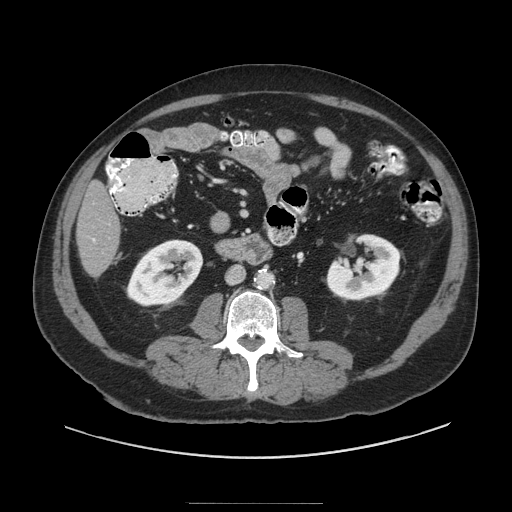
Contrast-enhanced abdominal CT (liver protocol), one axial slice; slice 22 of 91 in the series (ordered by position); soft-tissue window (W 400 / L 40 HU); 512 × 512 image matrix. From the clinical record (not read from this slice): diagnosis: hepatocellular carcinoma (patient treated with transarterial chemoembolisation; whether this scan precedes or follows treatment is not stated here); TNM stage (as recorded): Stage-I; Child-Pugh class: A.
Outlined on this slice (semi-automatically segmented with operator editing):
- liver parenchyma outside the tumour (the mass and vessels are separate outlines, so this box may not span the whole liver): bounding box (x1, y1, x2, y2) in pixels: (76, 180, 120, 276)
- liver vessels: (92, 238, 95, 242)